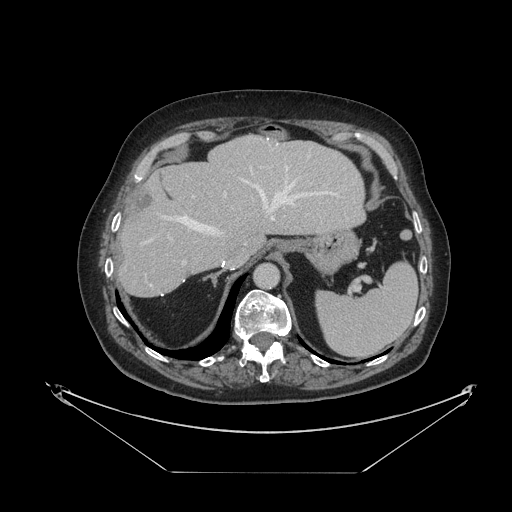
Contrast-enhanced abdominal CT, one axial slice. Slice 80 of 121 in the series (ordered by position). Reconstruction kernel STANDARD. 120 kVp. Soft-tissue window (W 400 / L 40 HU). 512 × 512 image matrix. Male patient, age 68 years. From the clinical record (not read from this slice): diagnosis: colorectal cancer liver metastases, imaged before liver resection; multiple liver metastases: no; largest metastasis: 4 cm; chemotherapy before resection: yes.
Annotated regions visible in this slice (manually delineated by an expert):
- hepatic veins: box from (x=143, y=144) to (x=339, y=244) px
- liver: (x=120, y=137)–(x=364, y=297)
- planned liver remnant (the part of the liver to remain after resection): (x=120, y=137)–(x=364, y=296)
- portal vein (with intrahepatic branches): (x=170, y=167)–(x=262, y=265)
- liver metastasis: (x=129, y=187)–(x=155, y=220)